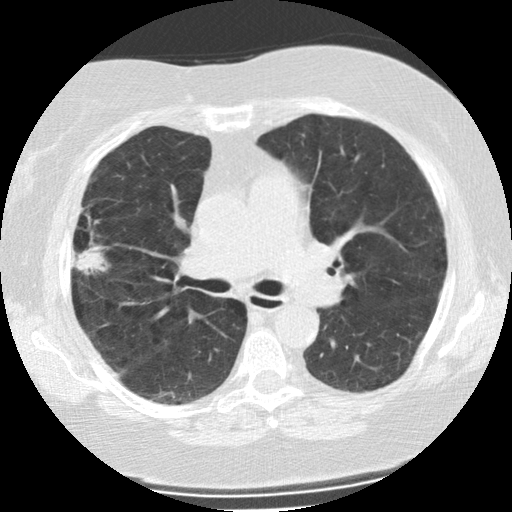
Axial slice from a low-dose chest CT screening exam. Second screening round (one year after baseline). Lung window (W 1500 / L -600 HU). 2.5 mm slice thickness. Standard (soft-tissue) reconstruction kernel (STANDARD). 512 × 512 image matrix. Female, age 73 years at enrolment. Former smoker at enrolment.
• Expert-annotated lung lesion, bounding box [x1, y1, x2, y2] px = [55, 210, 109, 282].
• The screening reader recorded 2 non-calcified nodules or masses ≥4 mm on this exam (right upper lobe, left upper lobe); which of them this box marks is not recorded.
• Official screen result: positive, change unspecified: nodule(s) >= 4 mm or enlarging nodule(s), mass(es), or other non-specific abnormalities suspicious for lung cancer.
• Participant outcome: lung cancer diagnosed 47 days after this screen — bronchiolo-alveolar adenocarcinoma, NOS, right upper lobe, moderately differentiated (G2), stage IIIB (AJCC 6th edition), 21 mm at pathology.